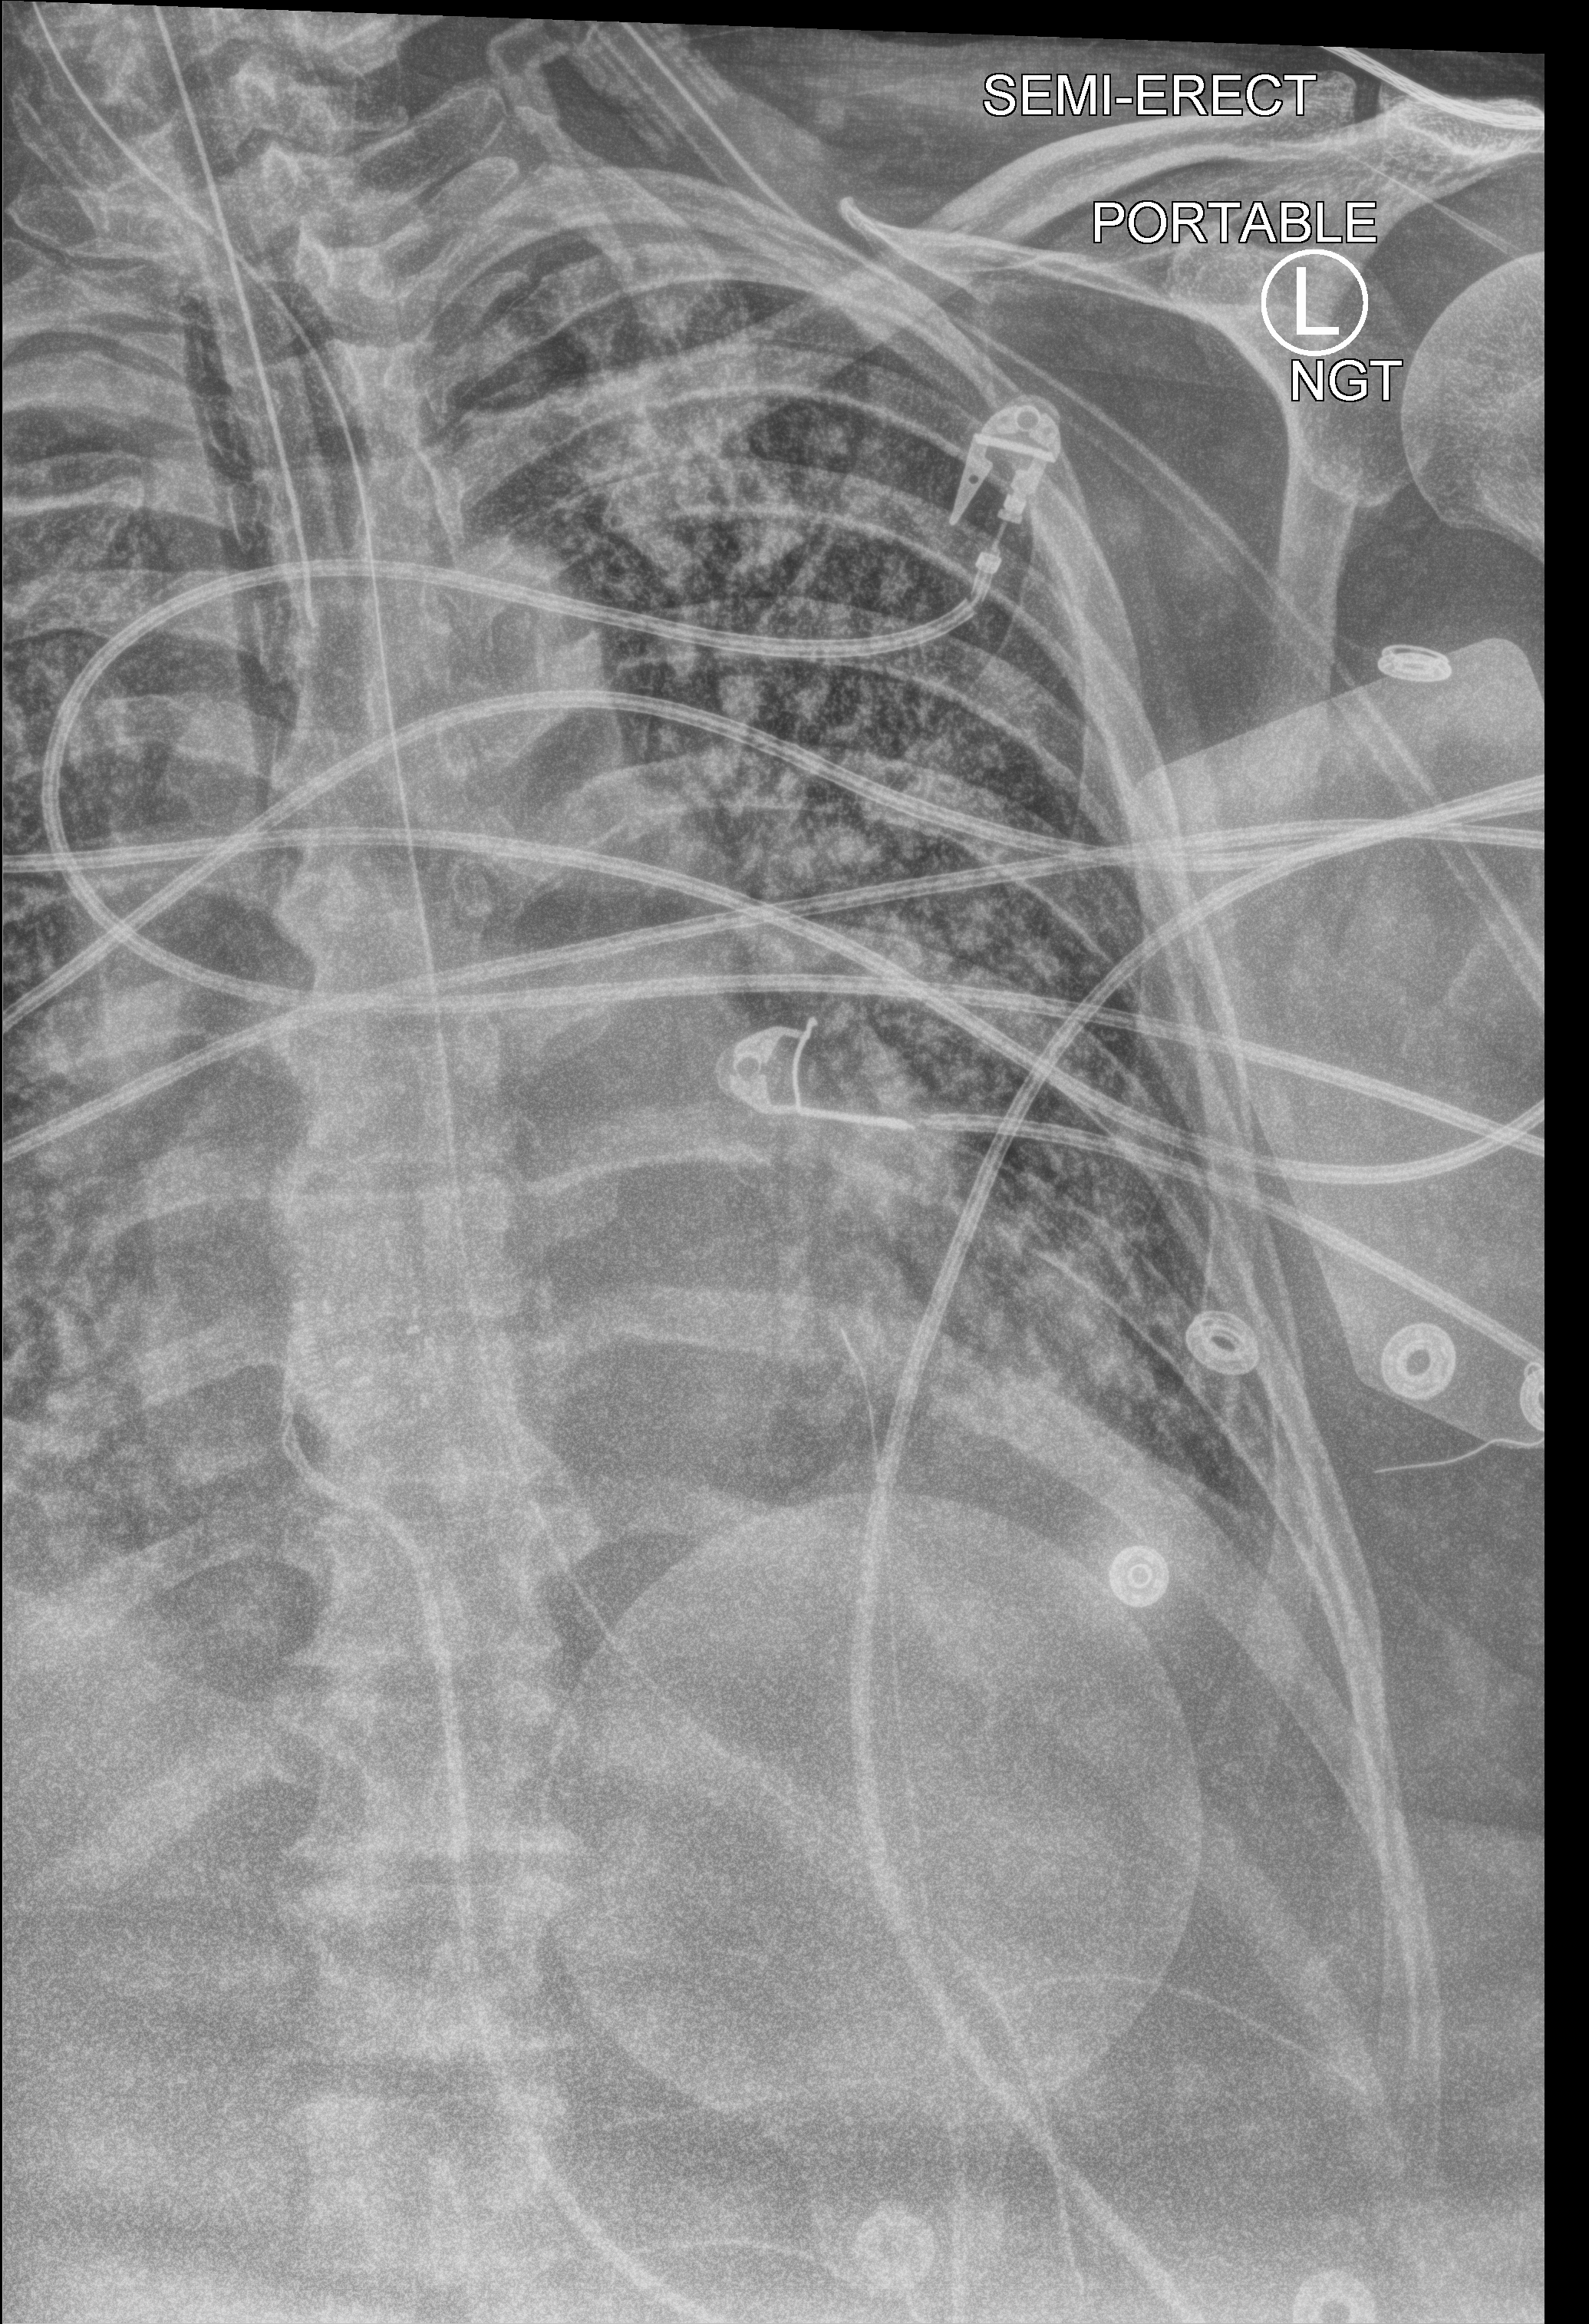
Chest X-ray (portable); anteroposterior (AP) projection. Patient hospitalised with COVID-19; male, aged 60–74 years.
Hospital-stay facts (about this admission, not read from this image; timing relative to this image not recorded): admitted to intensive care during this hospital stay: yes; length of hospital stay: 40 days; mechanically ventilated during this hospital stay: yes.